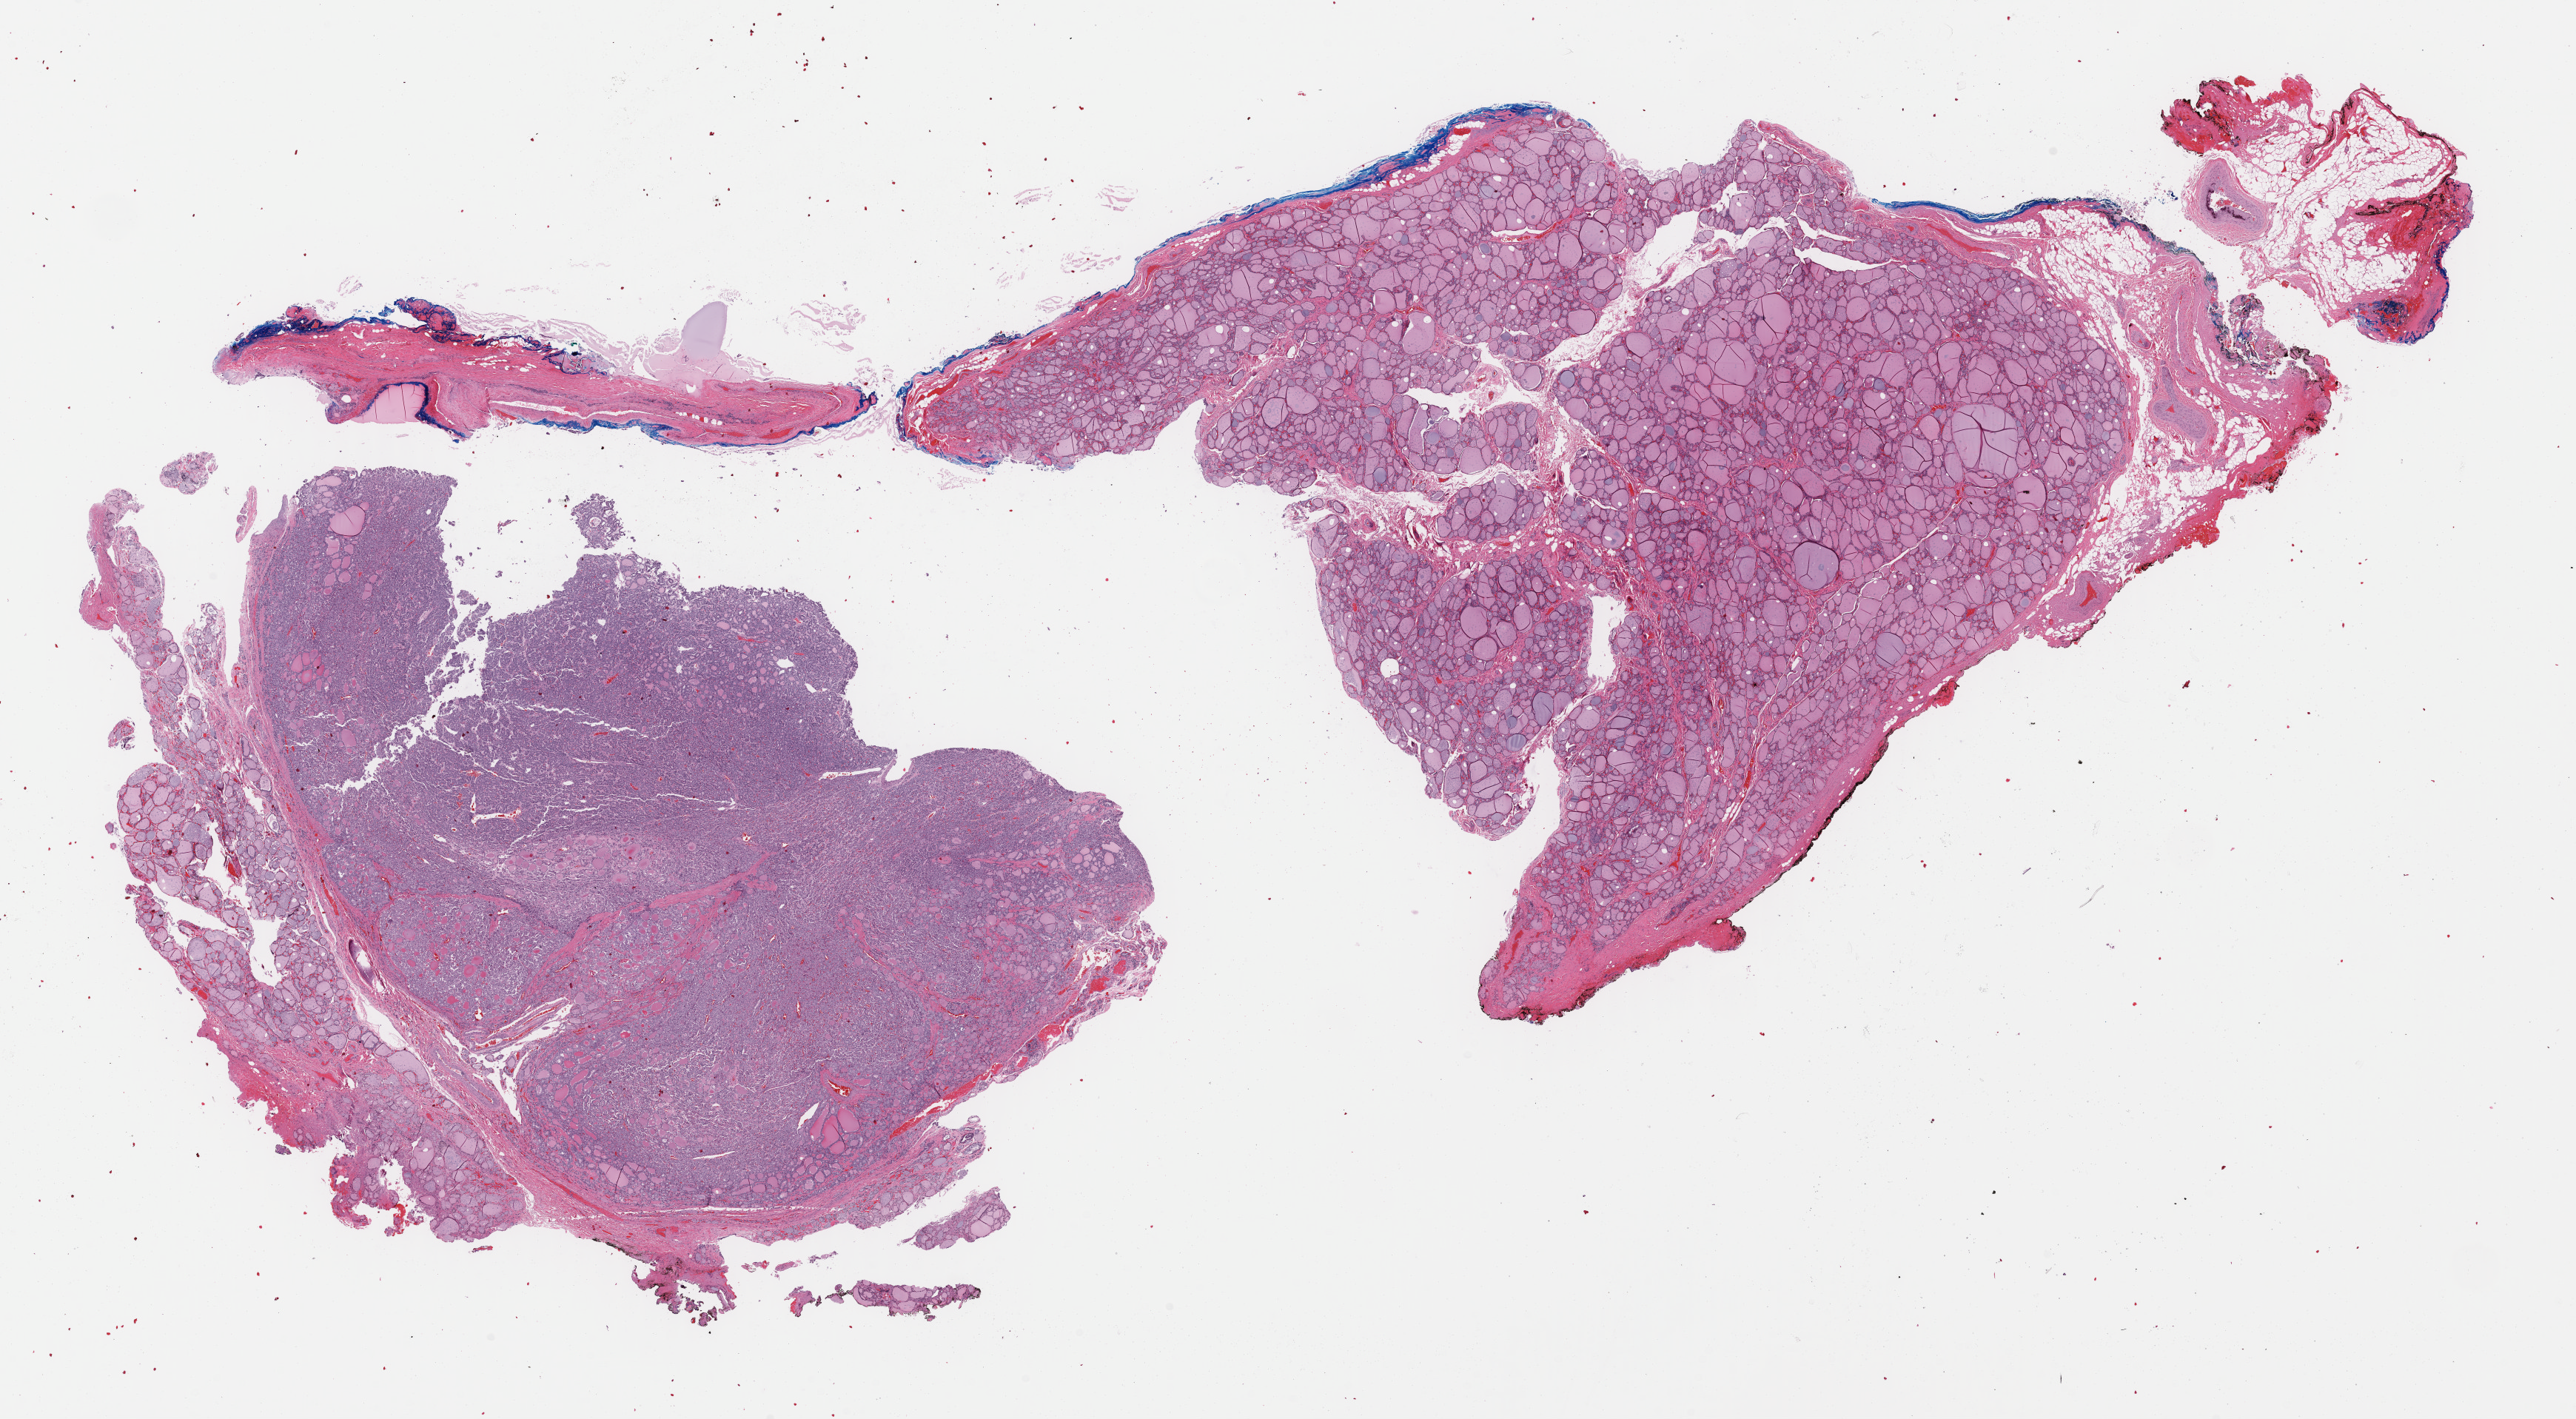
H&E-stained whole-slide image — a low-resolution overview of the entire scanned area, about 27.5 x 15.1 mm (acquisition: 40x scan). Formalin-fixed paraffin-embedded (FFPE) diagnostic section. Primary tumour sample from the thyroid. Patient: male, age at initial diagnosis 63 years.
* pathologic diagnosis: Papillary carcinoma, follicular variant (thyroid gland)
* lymph nodes positive (case pathology): 0 of 2 examined
* AJCC pathologic stage: III